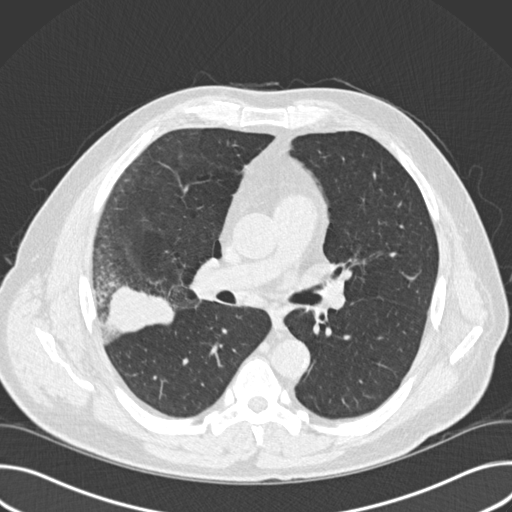
Low-dose screening chest CT, one axial slice; slice 93 of 157 in the series (ordered by position); reconstruction kernel B30f; 120 kVp; lung window (W 1500 / L -600 HU); 512 × 512 image matrix.
Outlined on this slice (manually delineated by an expert):
- lesion 1 (tumor, upper lobe of right lung): bounding box <104,285,174,334> (left, top, right, bottom; pixels)